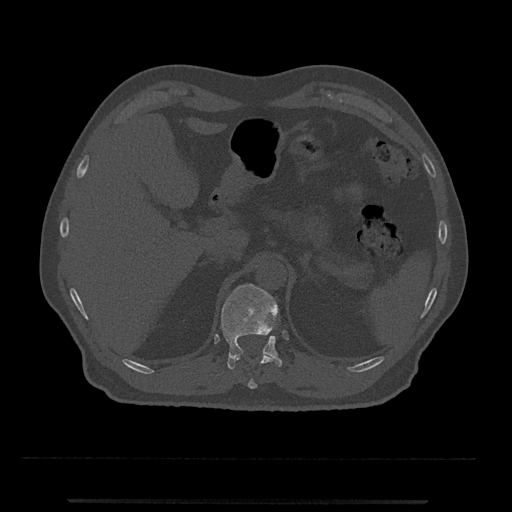
CT including the spine, one axial slice; slice 428 of 797 in the series (ordered by position); reconstruction kernel Br40s/3; 120 kVp; bone window (W 1800 / L 400 HU); 512 × 512 image matrix, field of view 419 × 419 mm. Male patient, age 63 years. From the clinical record (not read from this slice): primary cancer: prostate.
Outlined on this slice (semi-automatic segmentation, software-assisted and operator-edited):
- T11 vertebra: bounding box (x1, y1, x2, y2) in pixels: (235, 352, 274, 389)
- T12 vertebra: (221, 284, 282, 369)